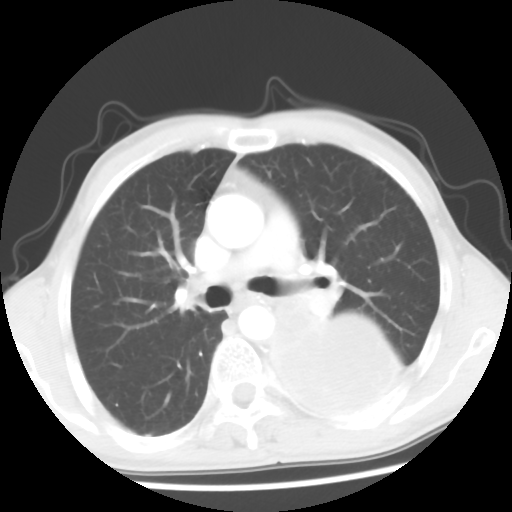
Chest CT, one axial slice. Position 35 of 56 along the scan axis. Lung window (W 1500 / L -600 HU). 512 × 512 image matrix, field of view 318 × 318 mm. Male patient, age 60 years. From the clinical record (not read from this slice): clinical TNM (as recorded): T4 N0 M0.
Structures marked on this image (bounding box drawn by a radiologist):
- lung tumour (recorded histology: squamous cell carcinoma): bounding box (x1, y1, x2, y2) in pixels: (256, 282, 419, 442)